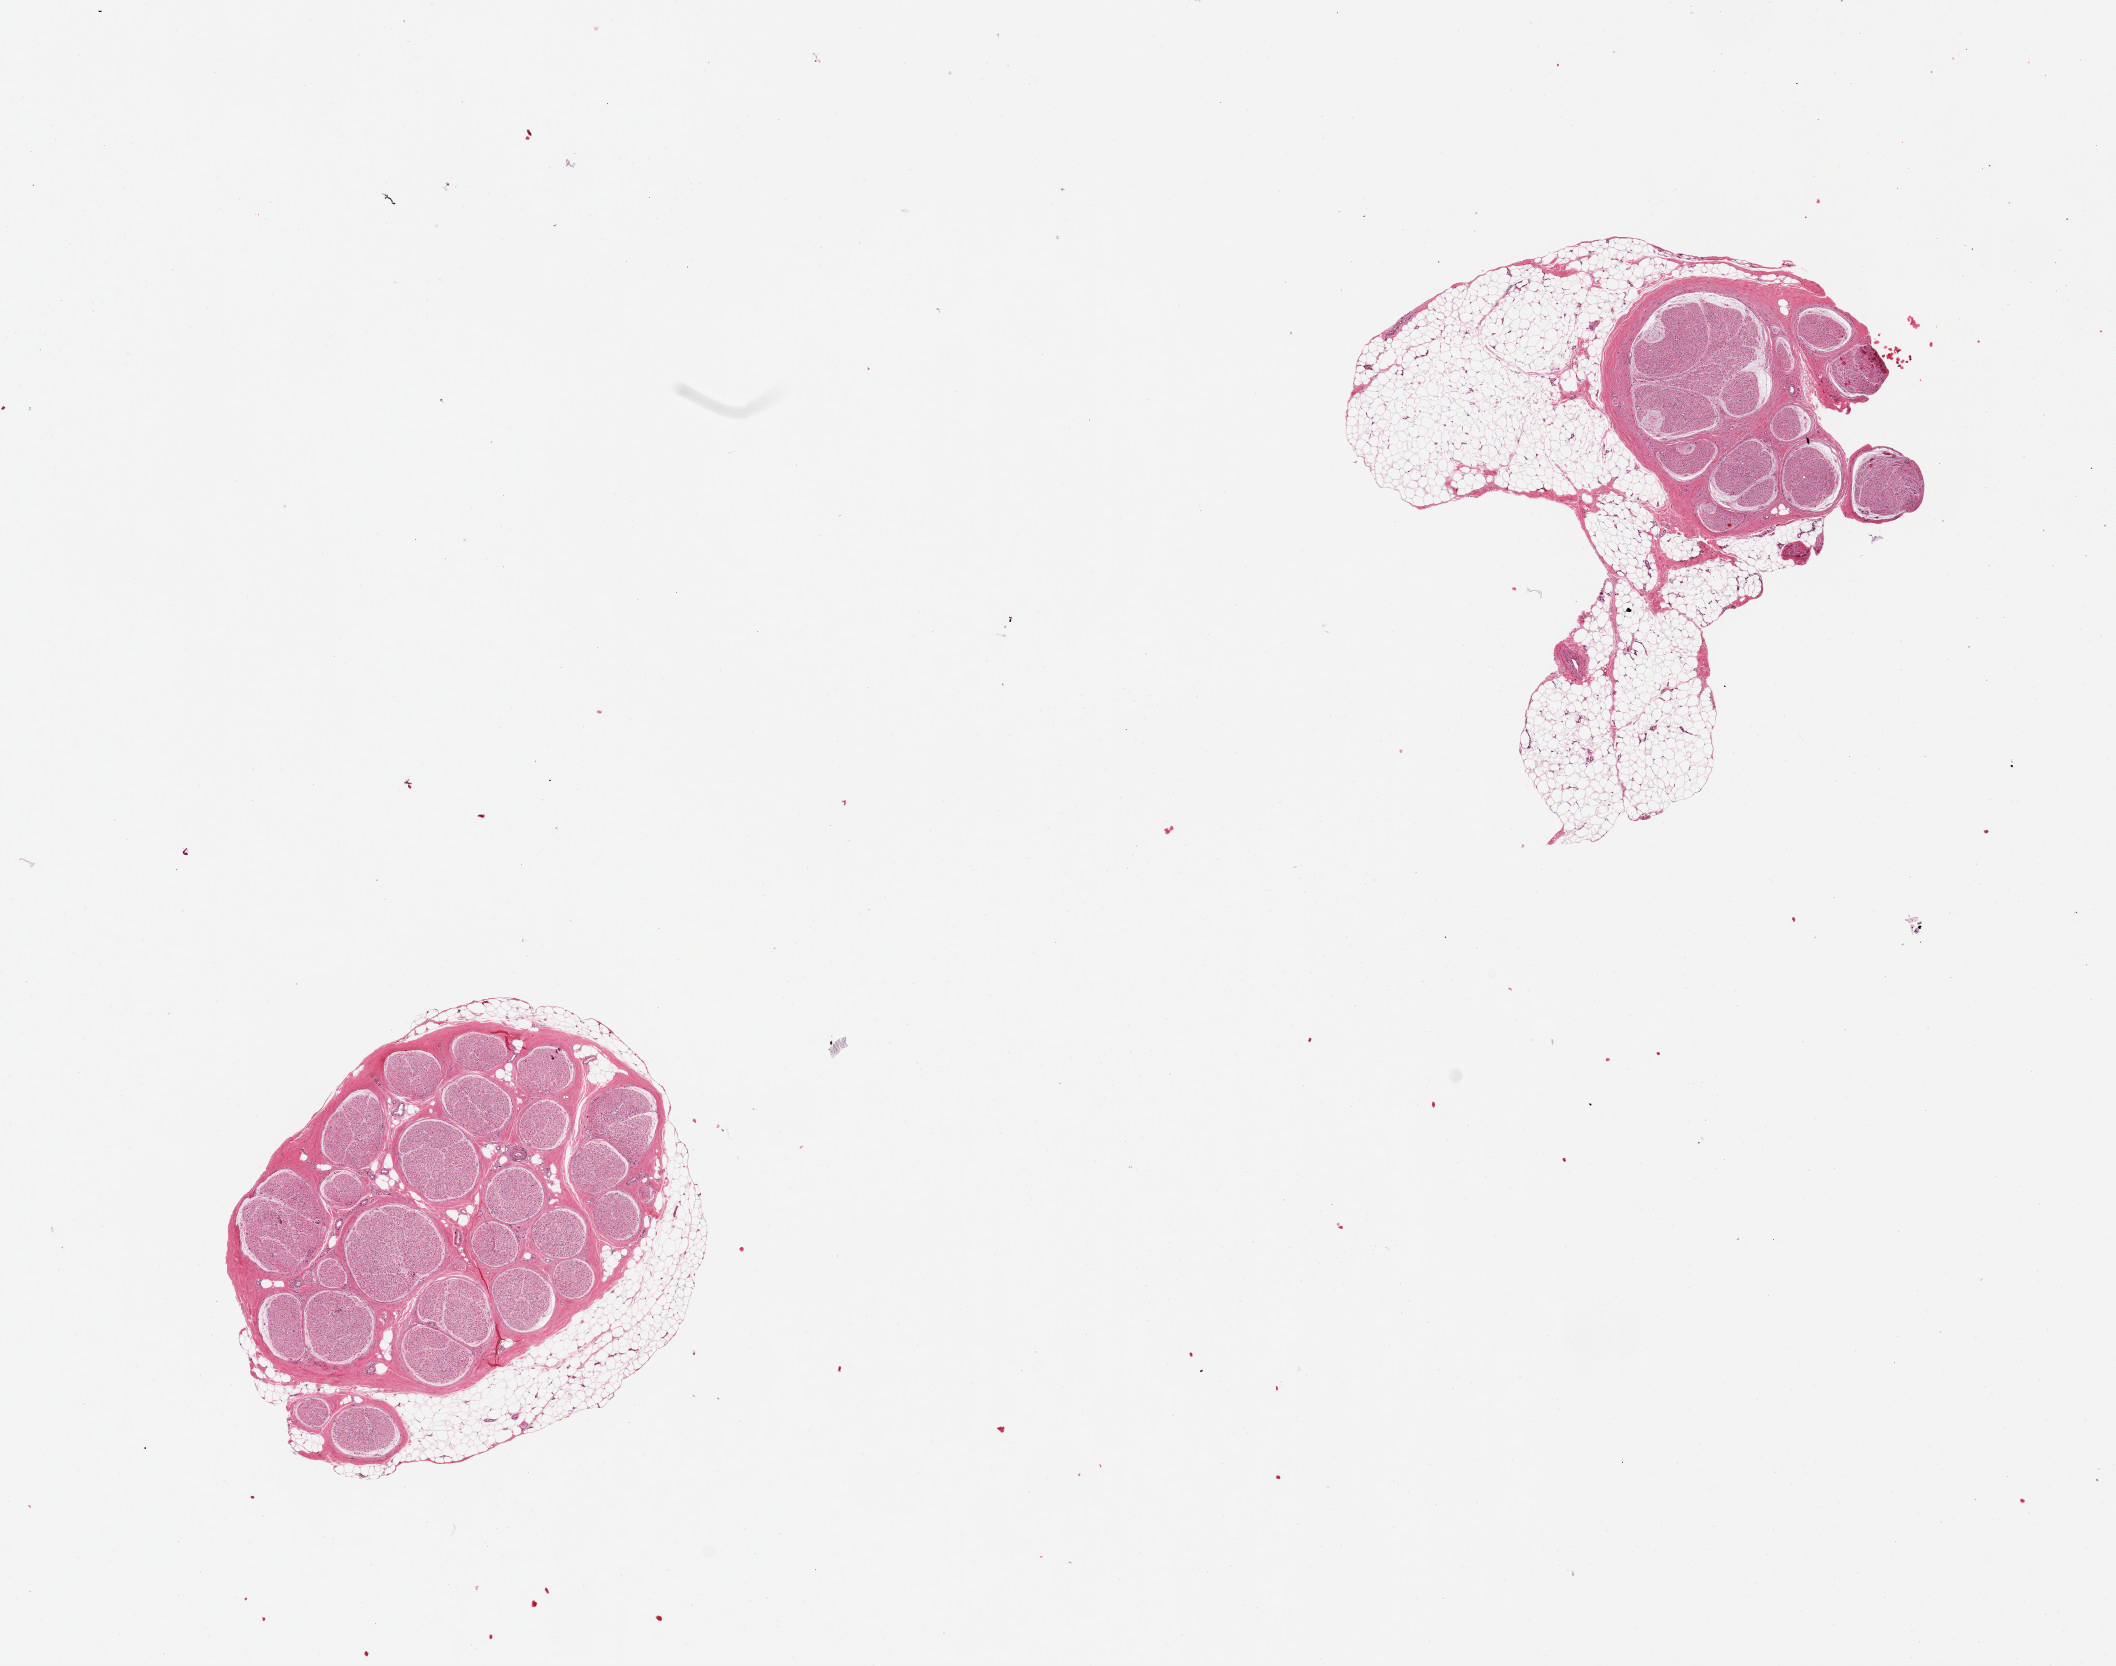
Whole-slide image, hematoxylin and eosin (H&E) stain, shown as a low-resolution overview of the whole scanned area (about 16.7 x 13.2 mm, from a 20x scan), PAXgene-fixed paraffin-embedded (PFPE) section, target tissue: tibial nerve, tissue donor sample. Donor sex: female.
* reviewer comment on this tissue sample: 2 pieces, prominent adherent fat on both, 0.5-2mm